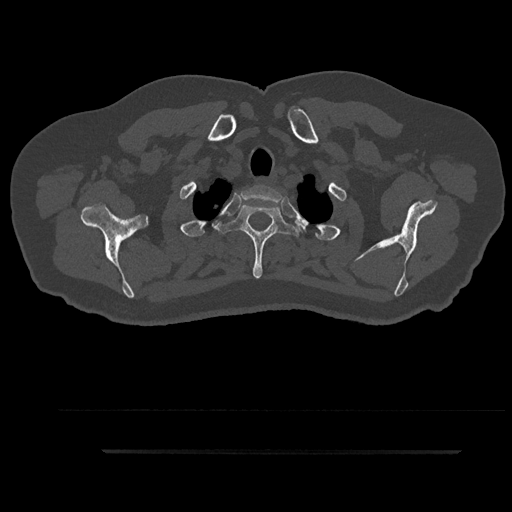
CT including the spine, one axial slice; reconstruction kernel Br40s/3; bone window (W 1800 / L 400 HU); 0.5 mm slice thickness; 512 × 512 image matrix. Patient: male, 63 years. Case-level facts recorded for this patient, not image findings: primary cancer: renal.
Structures marked on this image (semi-automatically segmented with operator editing):
- T1 vertebra: bounding box (x1, y1, x2, y2) in pixels: (238, 185, 283, 218)
- T2 vertebra: (215, 204, 303, 279)